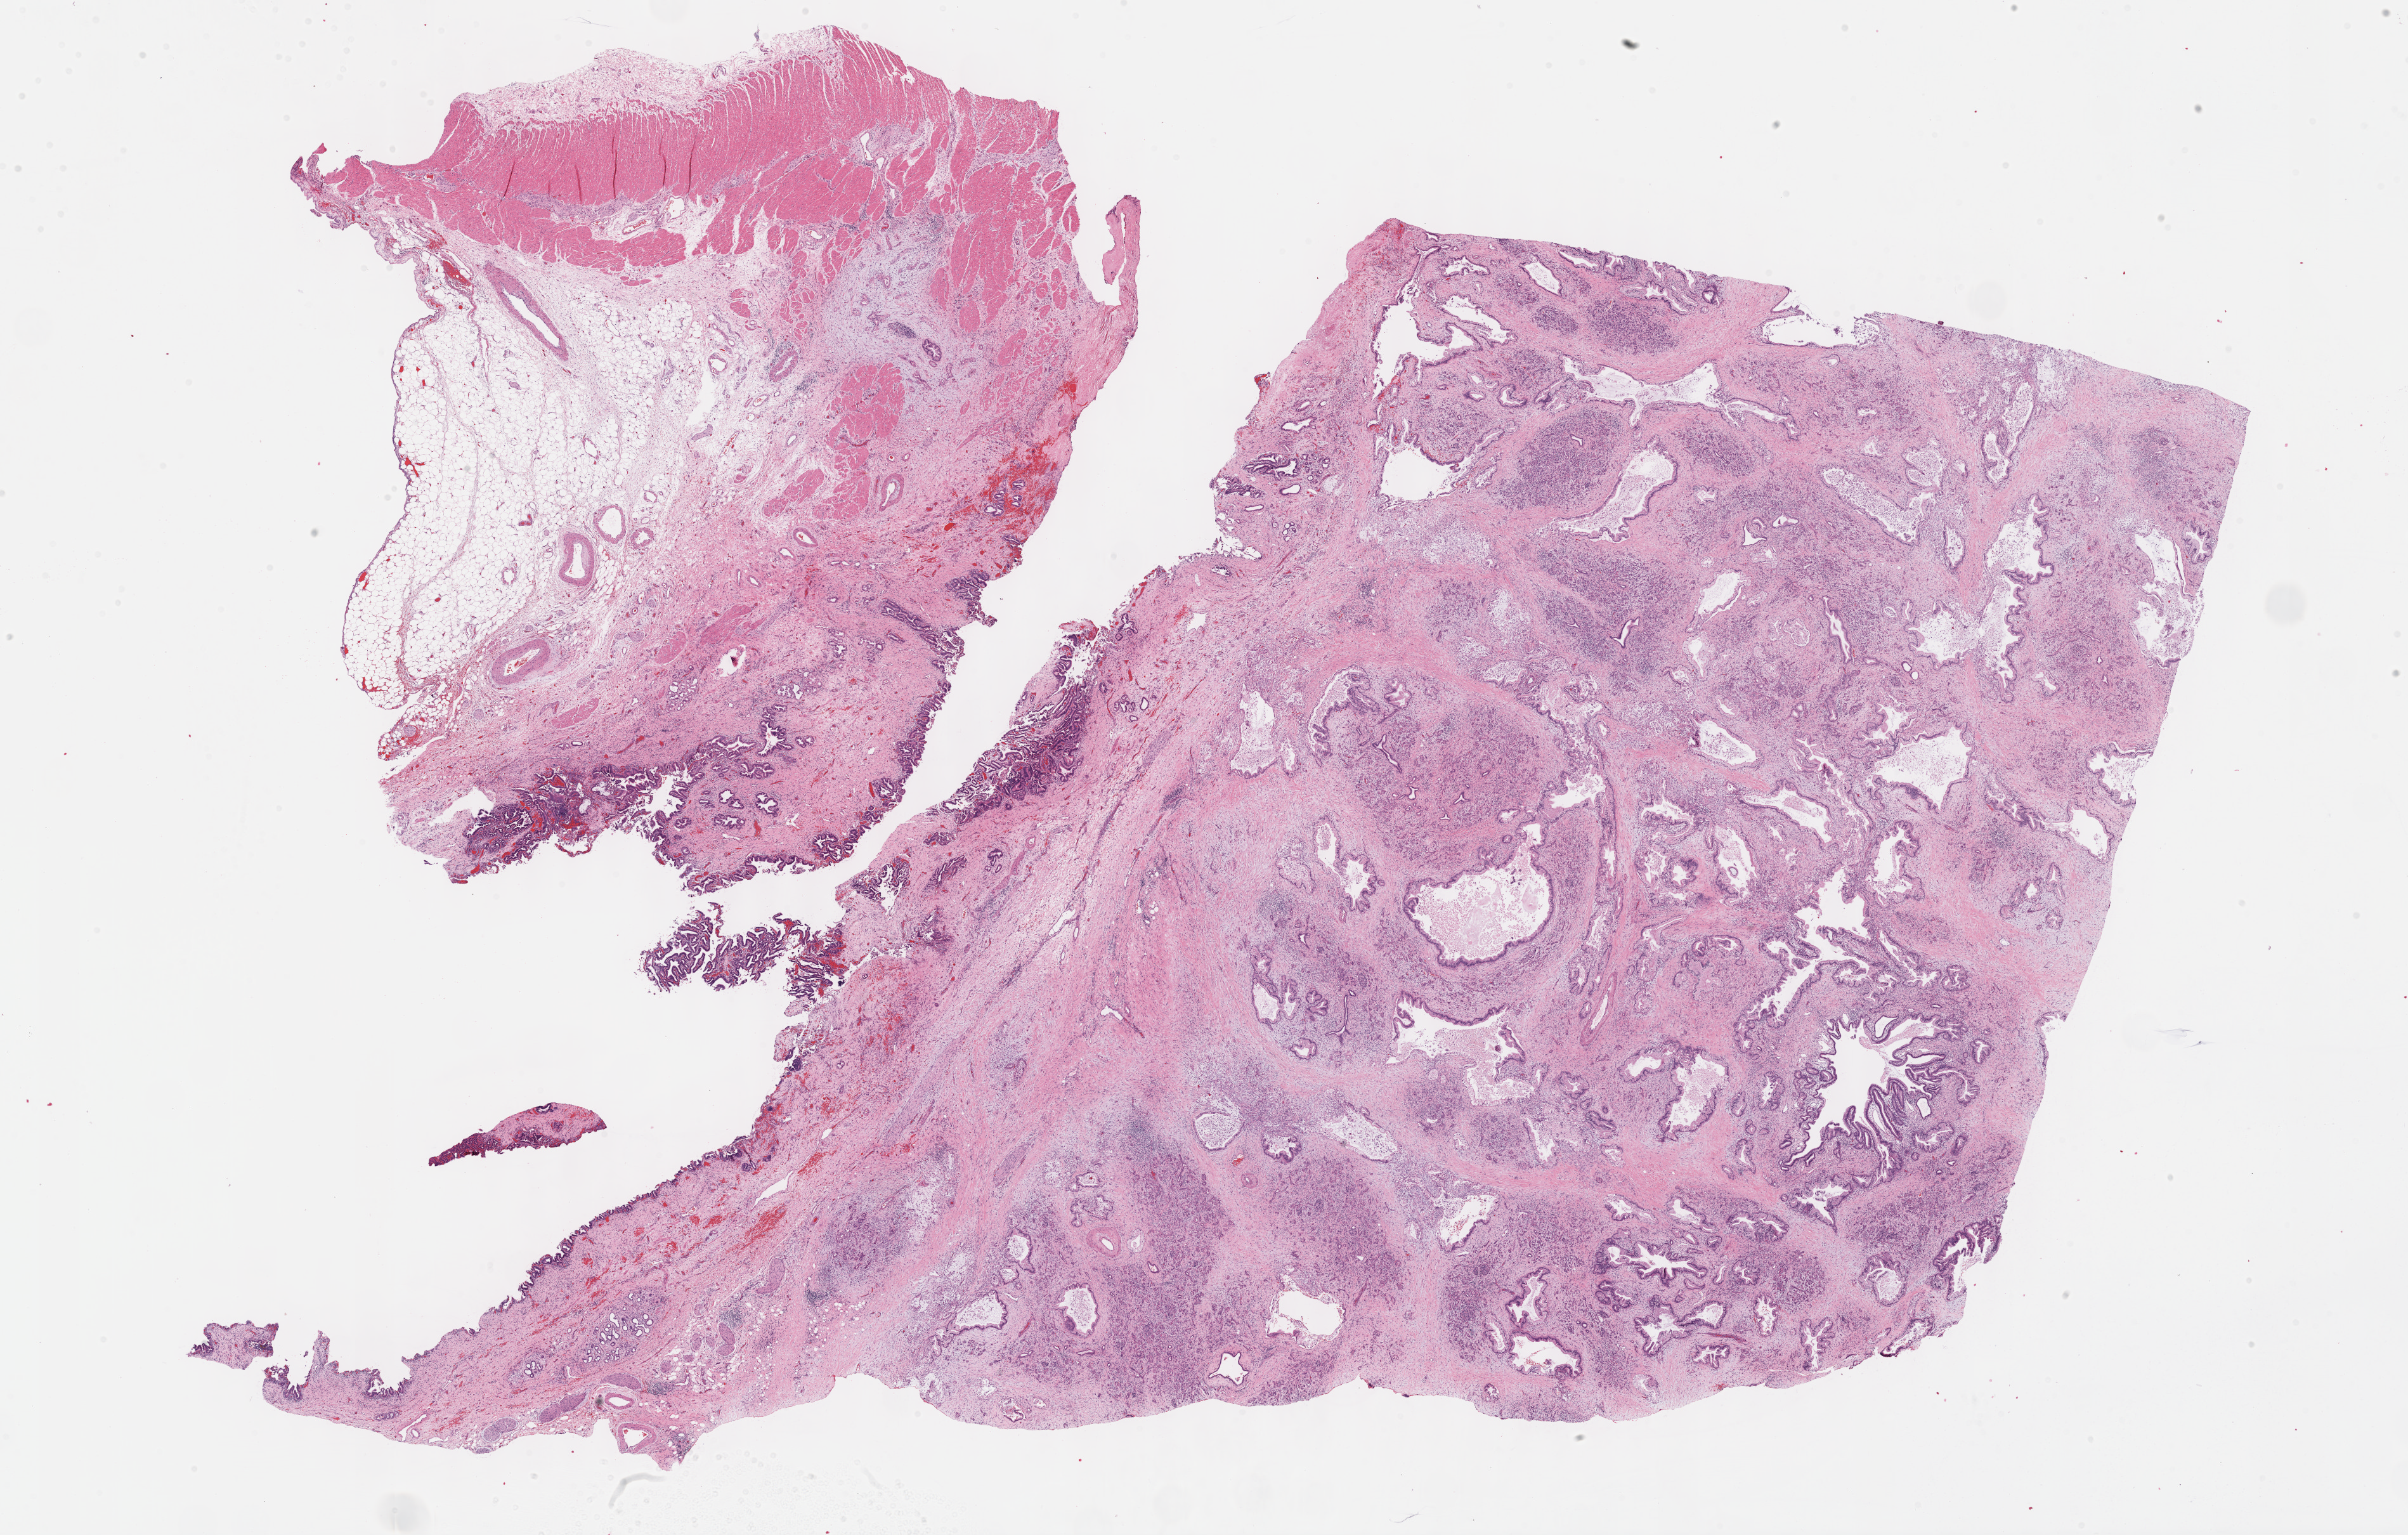
Whole-slide histology image, Hematoxylin and eosin (H&E) stained, a low-resolution overview of the entire scanned area, about 30.7 x 19.6 mm (acquisition: 40x scan); formalin-fixed paraffin-embedded (FFPE) diagnostic section; pancreas, primary tumour sample. Patient: male, age at initial diagnosis 67 years. Histologic grade: G3 (poorly differentiated).
- diagnosis: Infiltrating duct carcinoma, NOS
- AJCC pathologic stage: IIB (7th edition)
- lymph nodes positive (case pathology): 1 of 9 examined